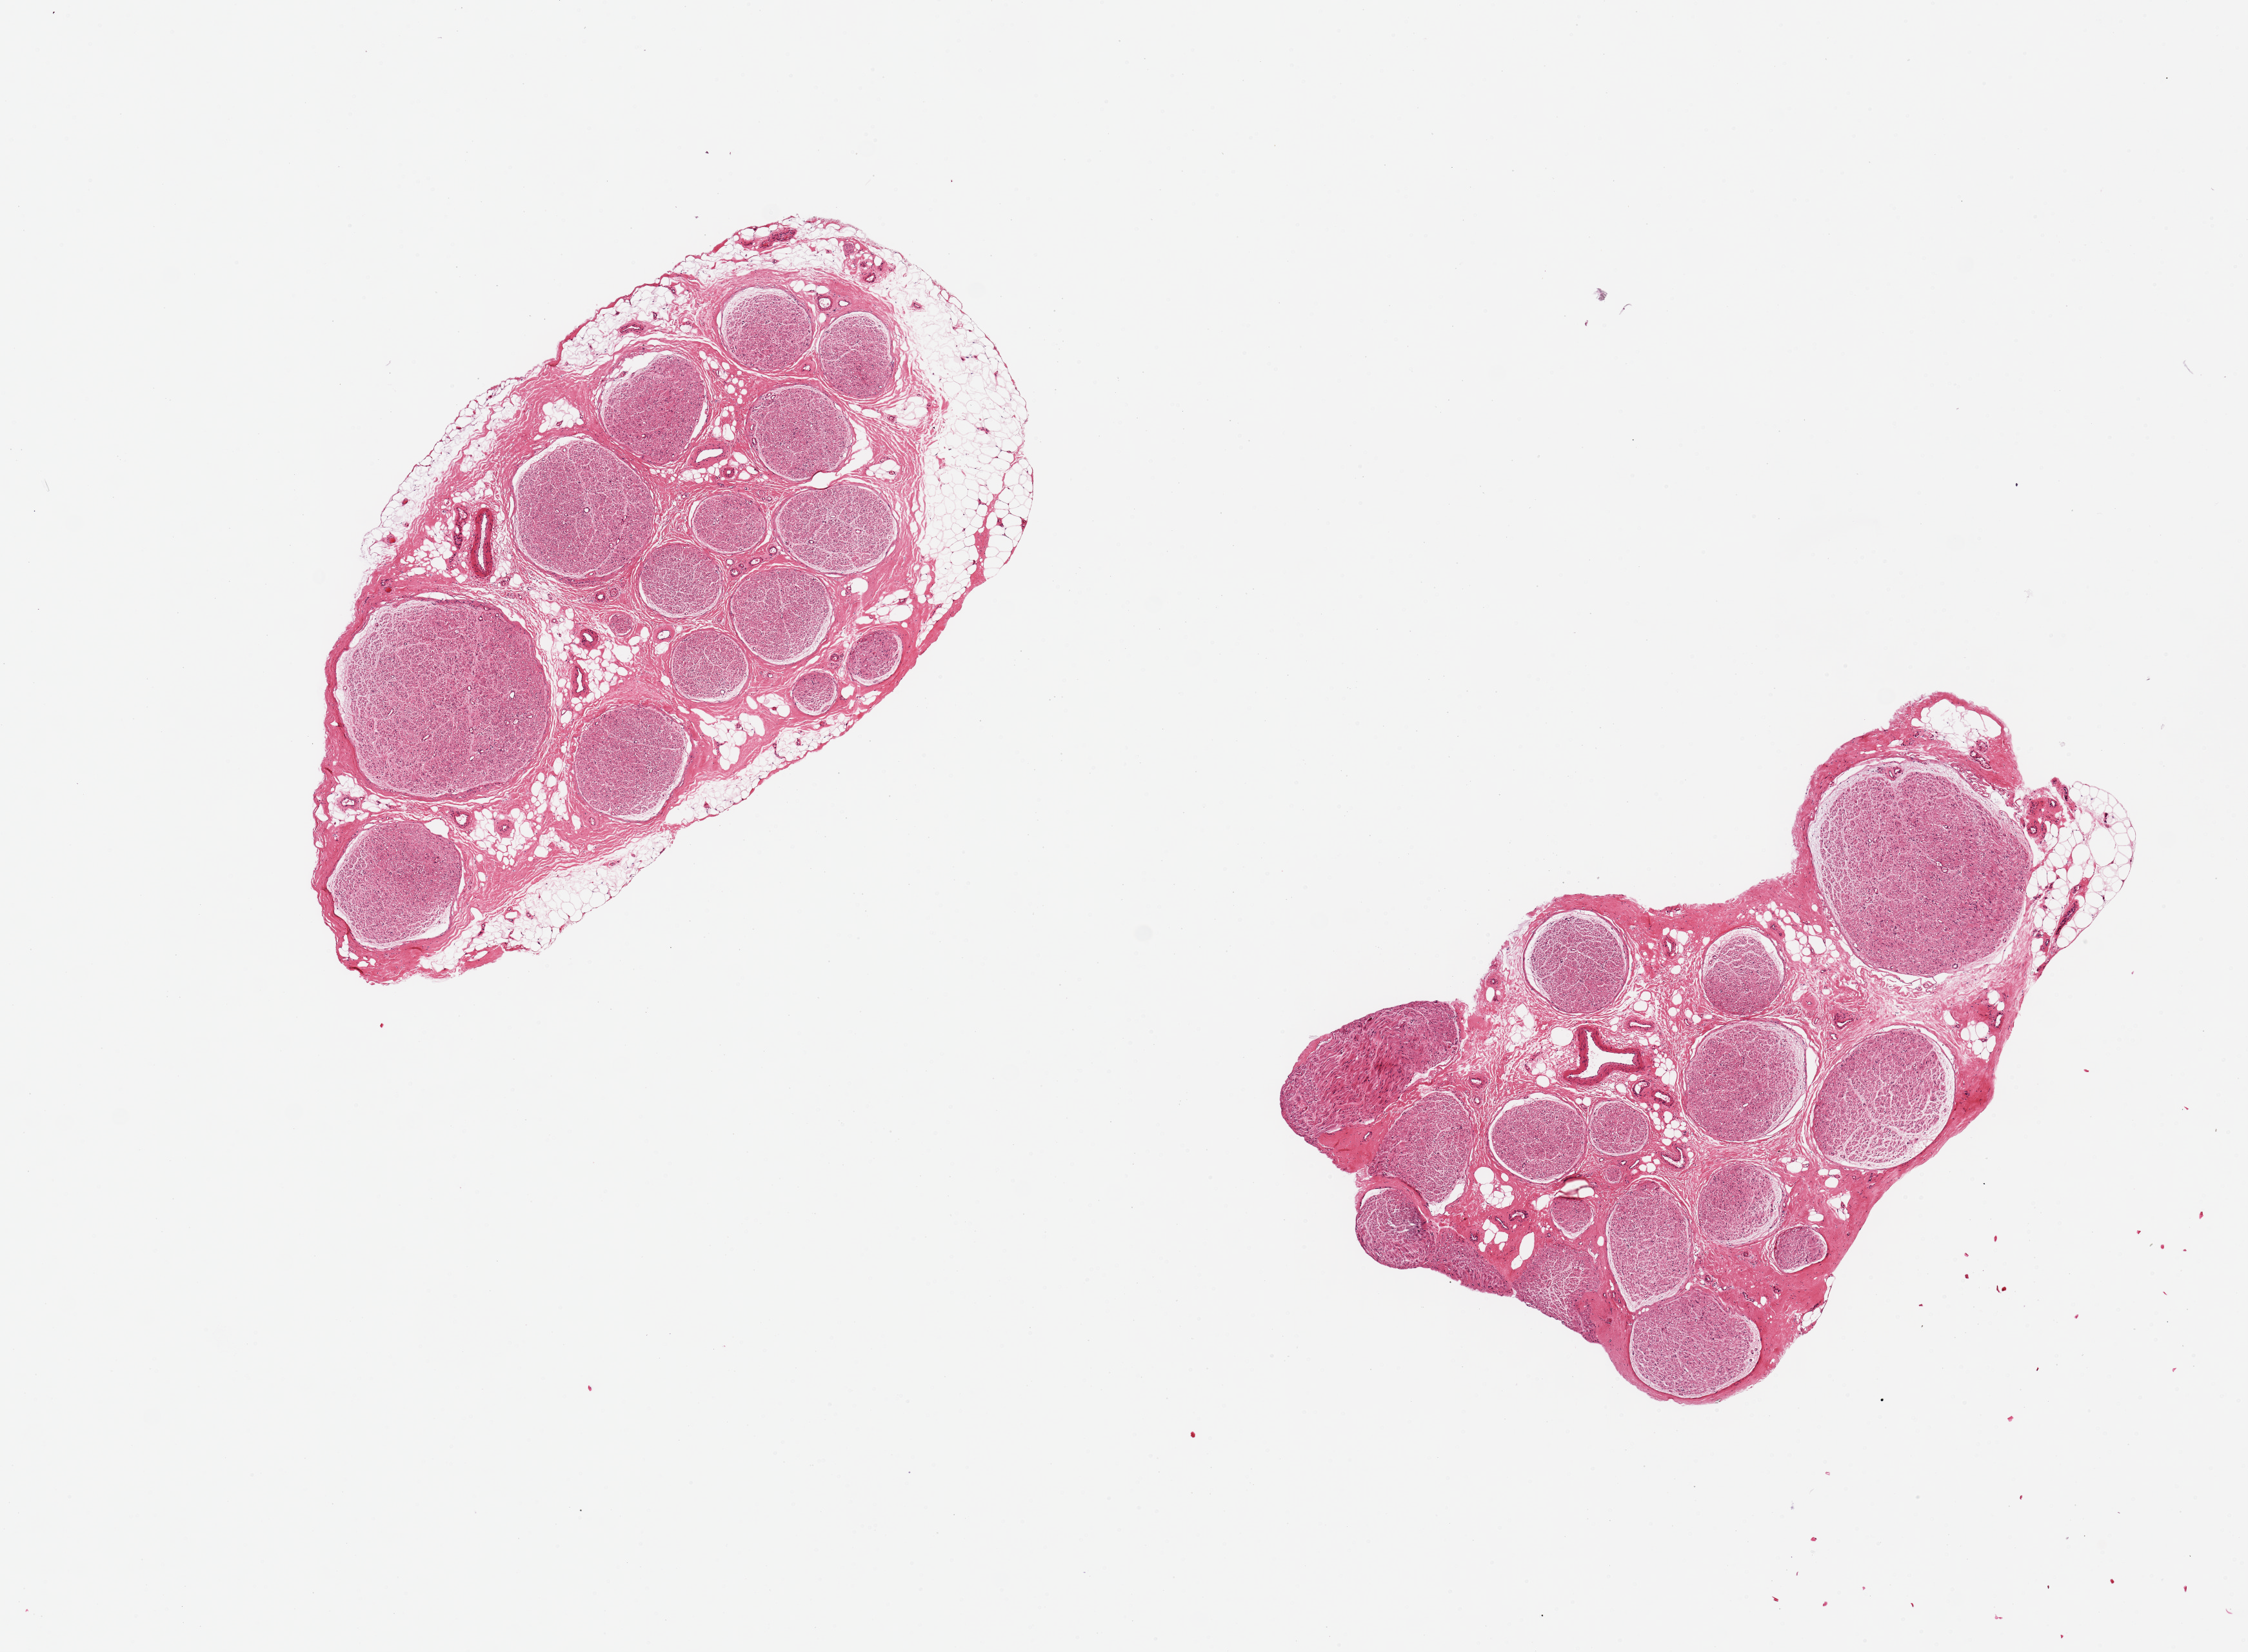
Digitized H&E-stained section, brightfield, shown as a low-resolution overview of the whole scanned area (about 13.8 x 10.1 mm). PAXgene-fixed, paraffin-embedded tissue. Section of tibial nerve (target tissue). Tissue donor sample.
Pathologist's review note for this sample: 2 pieces, 5.5x3 & 5x3.5mm; Up to 20% internal and extraneous adipose.